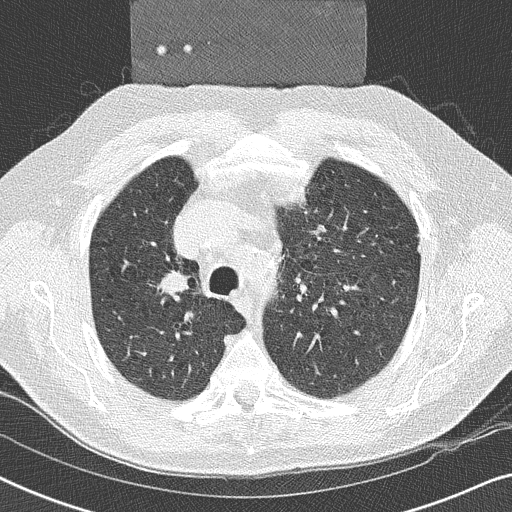
Chest CT (low-dose screening protocol), one axial image; second screening round (one year after baseline); lung window (W 1500 / L -600 HU); lung (sharp) reconstruction kernel (B50f); slice 75 of 252 in the series; 512 × 512 image matrix. Male participant, aged 59 years at enrolment. Former smoker at enrolment.
Expert reader's lesion annotation, box from (x=147, y=258) to (x=205, y=308) px. Reader record for this screening exam (exam-level; its link to the box is not recorded): non-calcified nodule or mass ≥4 mm, right upper lobe, 17 × 16 mm, smooth margins, soft tissue attenuation, pre-existing on the prior screen: yes. Official screen result: positive, other. Participant outcome: lung cancer diagnosed 14 days after this screen — squamous cell carcinoma, NOS, right upper lobe, poorly differentiated (G3), stage IIA (AJCC 6th edition), 20 mm at pathology.